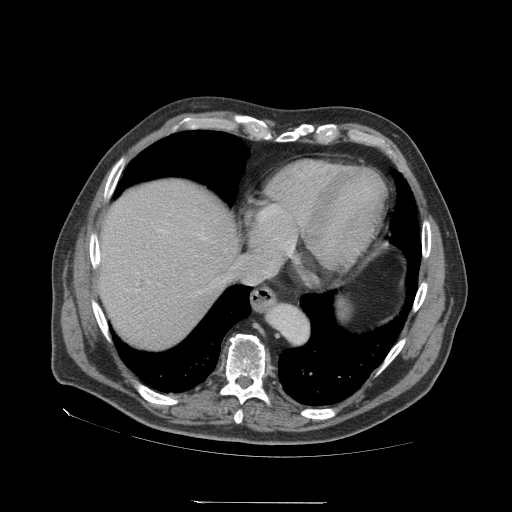
Contrast-enhanced abdominal CT (liver protocol), one axial slice; position 63 of 83 along the scan axis; soft-tissue window (W 400 / L 40 HU); 2.5 mm slice thickness; 512 × 512 image matrix, field of view 460 × 460 mm. From the clinical record (not read from this slice): diagnosis: hepatocellular carcinoma (patient treated with transarterial chemoembolisation; whether this scan precedes or follows treatment is not stated here); TNM stage (as recorded): Stage-I; Child-Pugh class: A; tumour differentiation: well differentiated.
Outlined on this slice (semi-automatic segmentation, software-assisted and operator-edited):
- abdominal aorta: bounding box (x1, y1, x2, y2) in pixels: (269, 306, 307, 341)
- liver parenchyma outside the tumour (the mass and vessels are separate outlines, so this box may not span the whole liver): (98, 180, 238, 348)
- liver vessels: (136, 230, 205, 291)